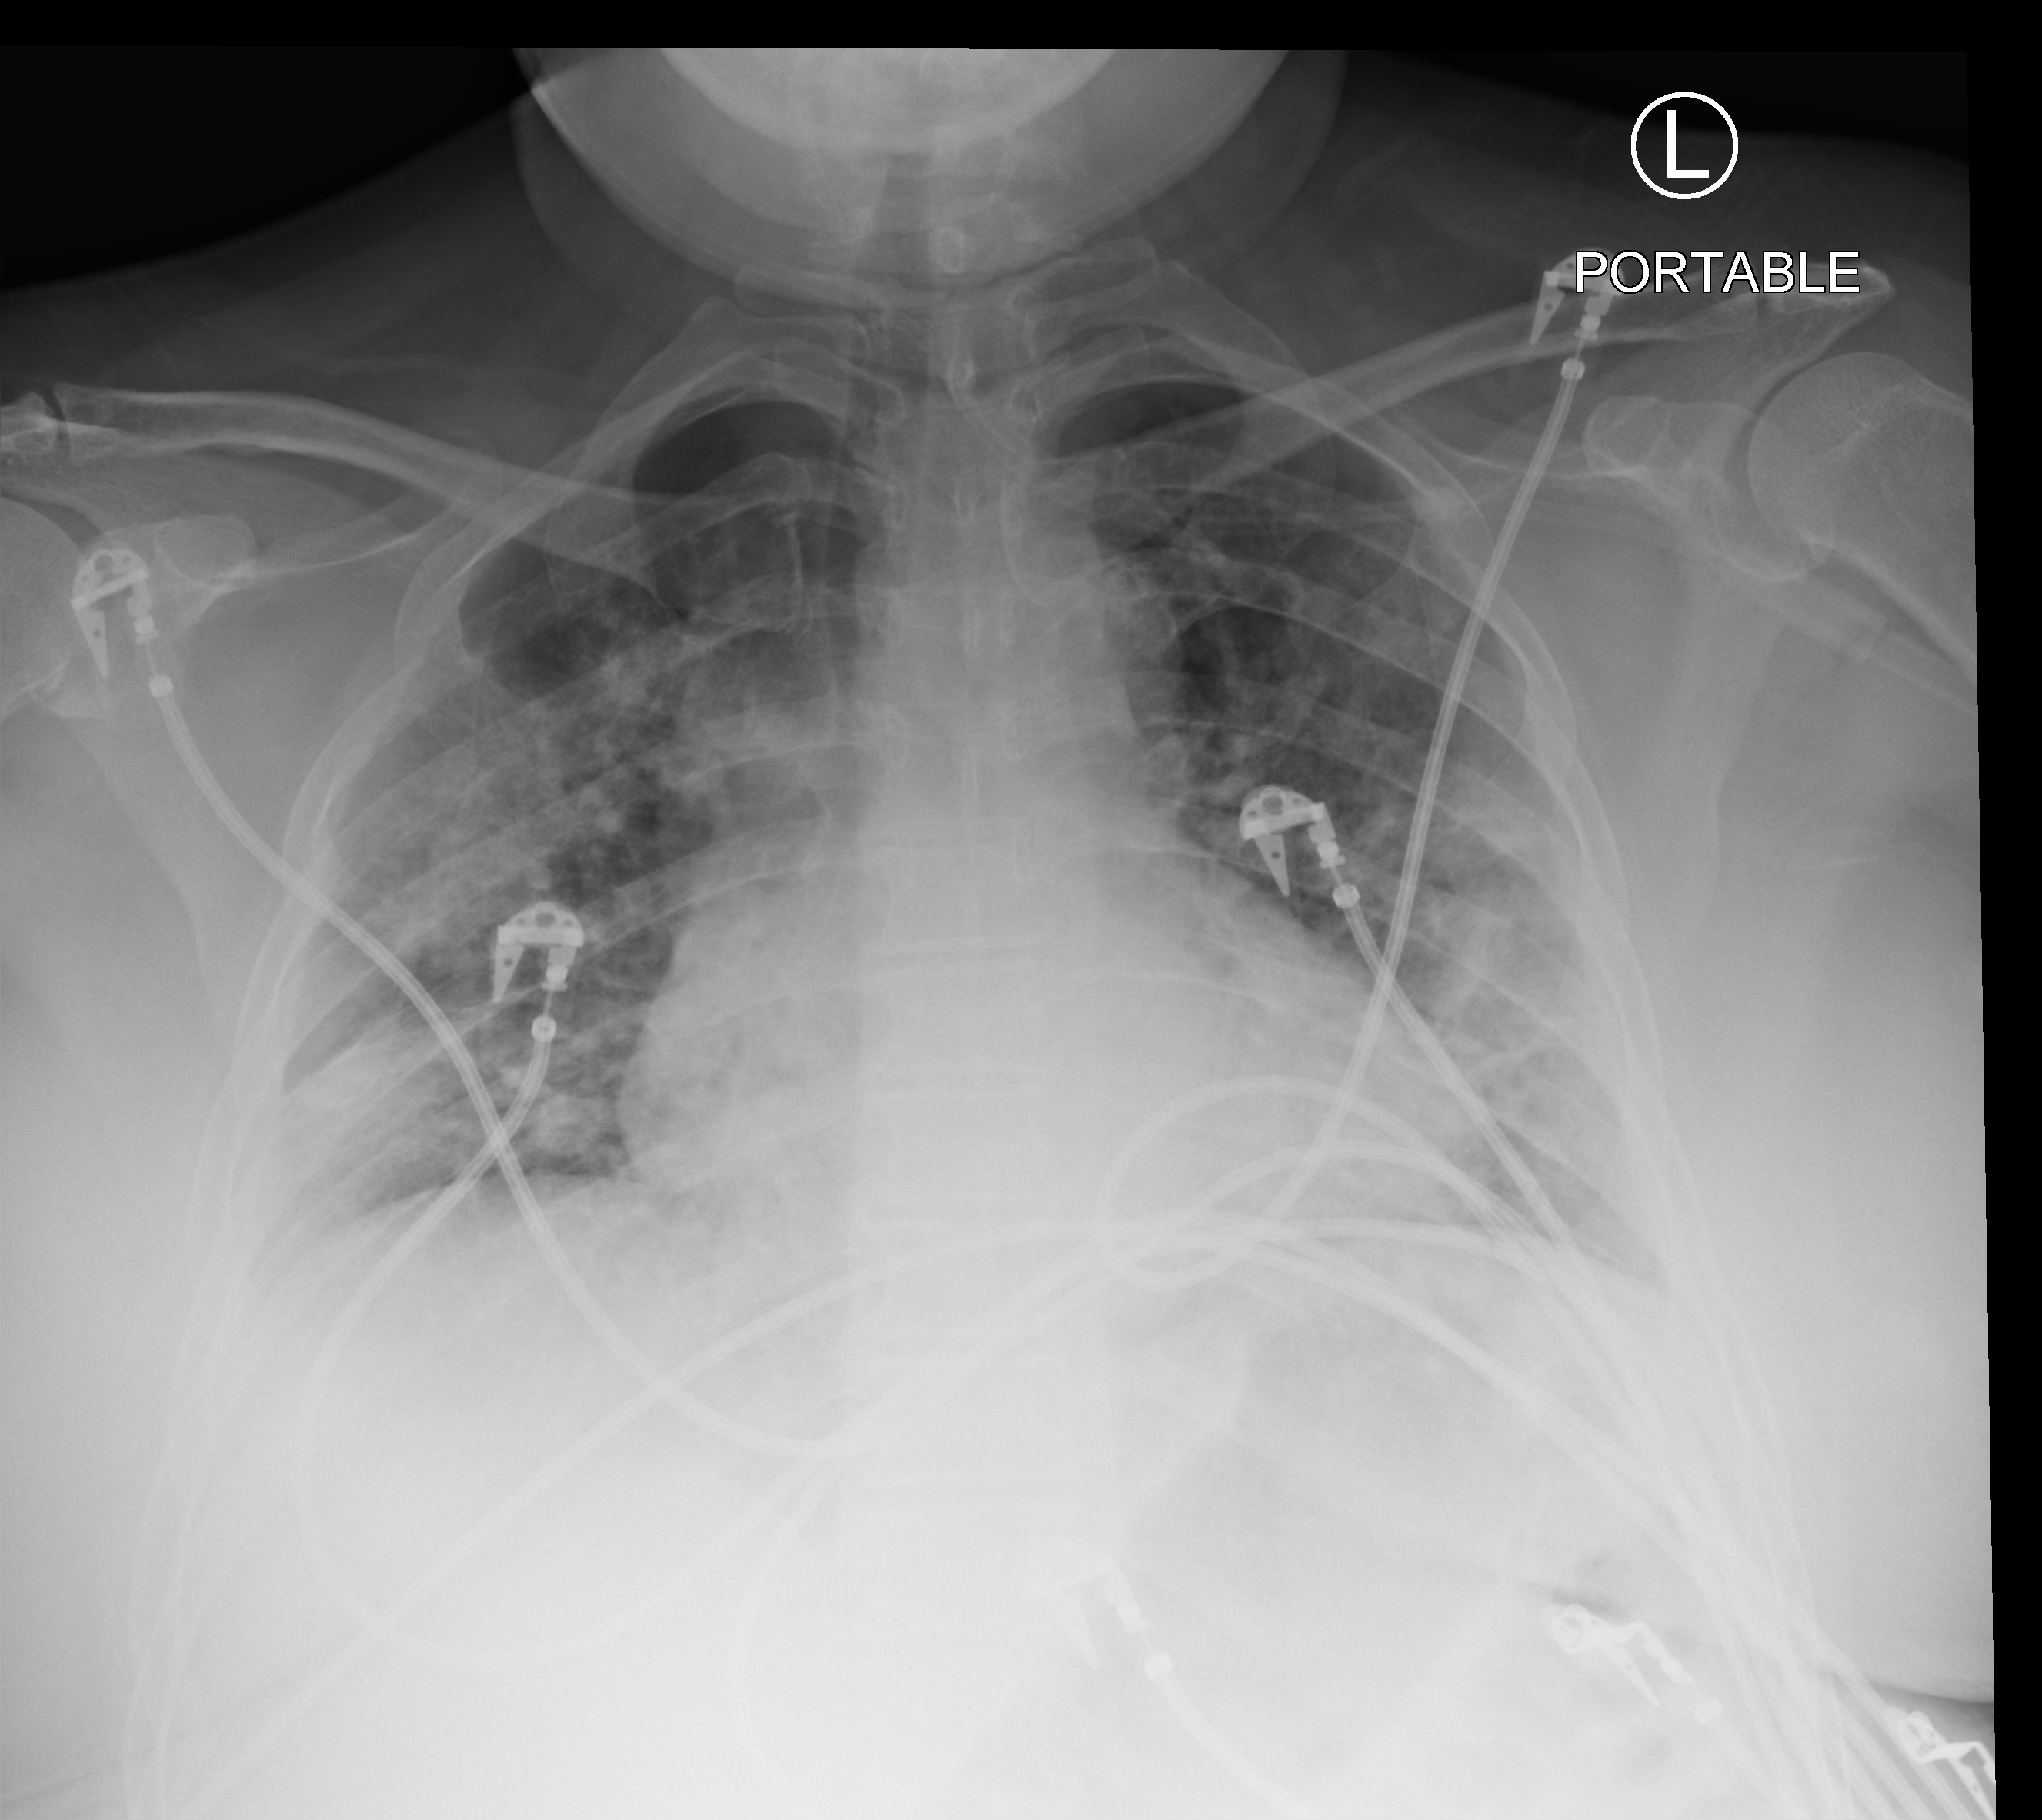
Chest X-ray (portable), anteroposterior (AP) projection. Female patient hospitalised with COVID-19, age 18–59 years.
Admission-level facts for this patient (not findings on this image; timing relative to this image not recorded):
- length of hospital stay: 21 days
- admitted to intensive care during this hospital stay: no